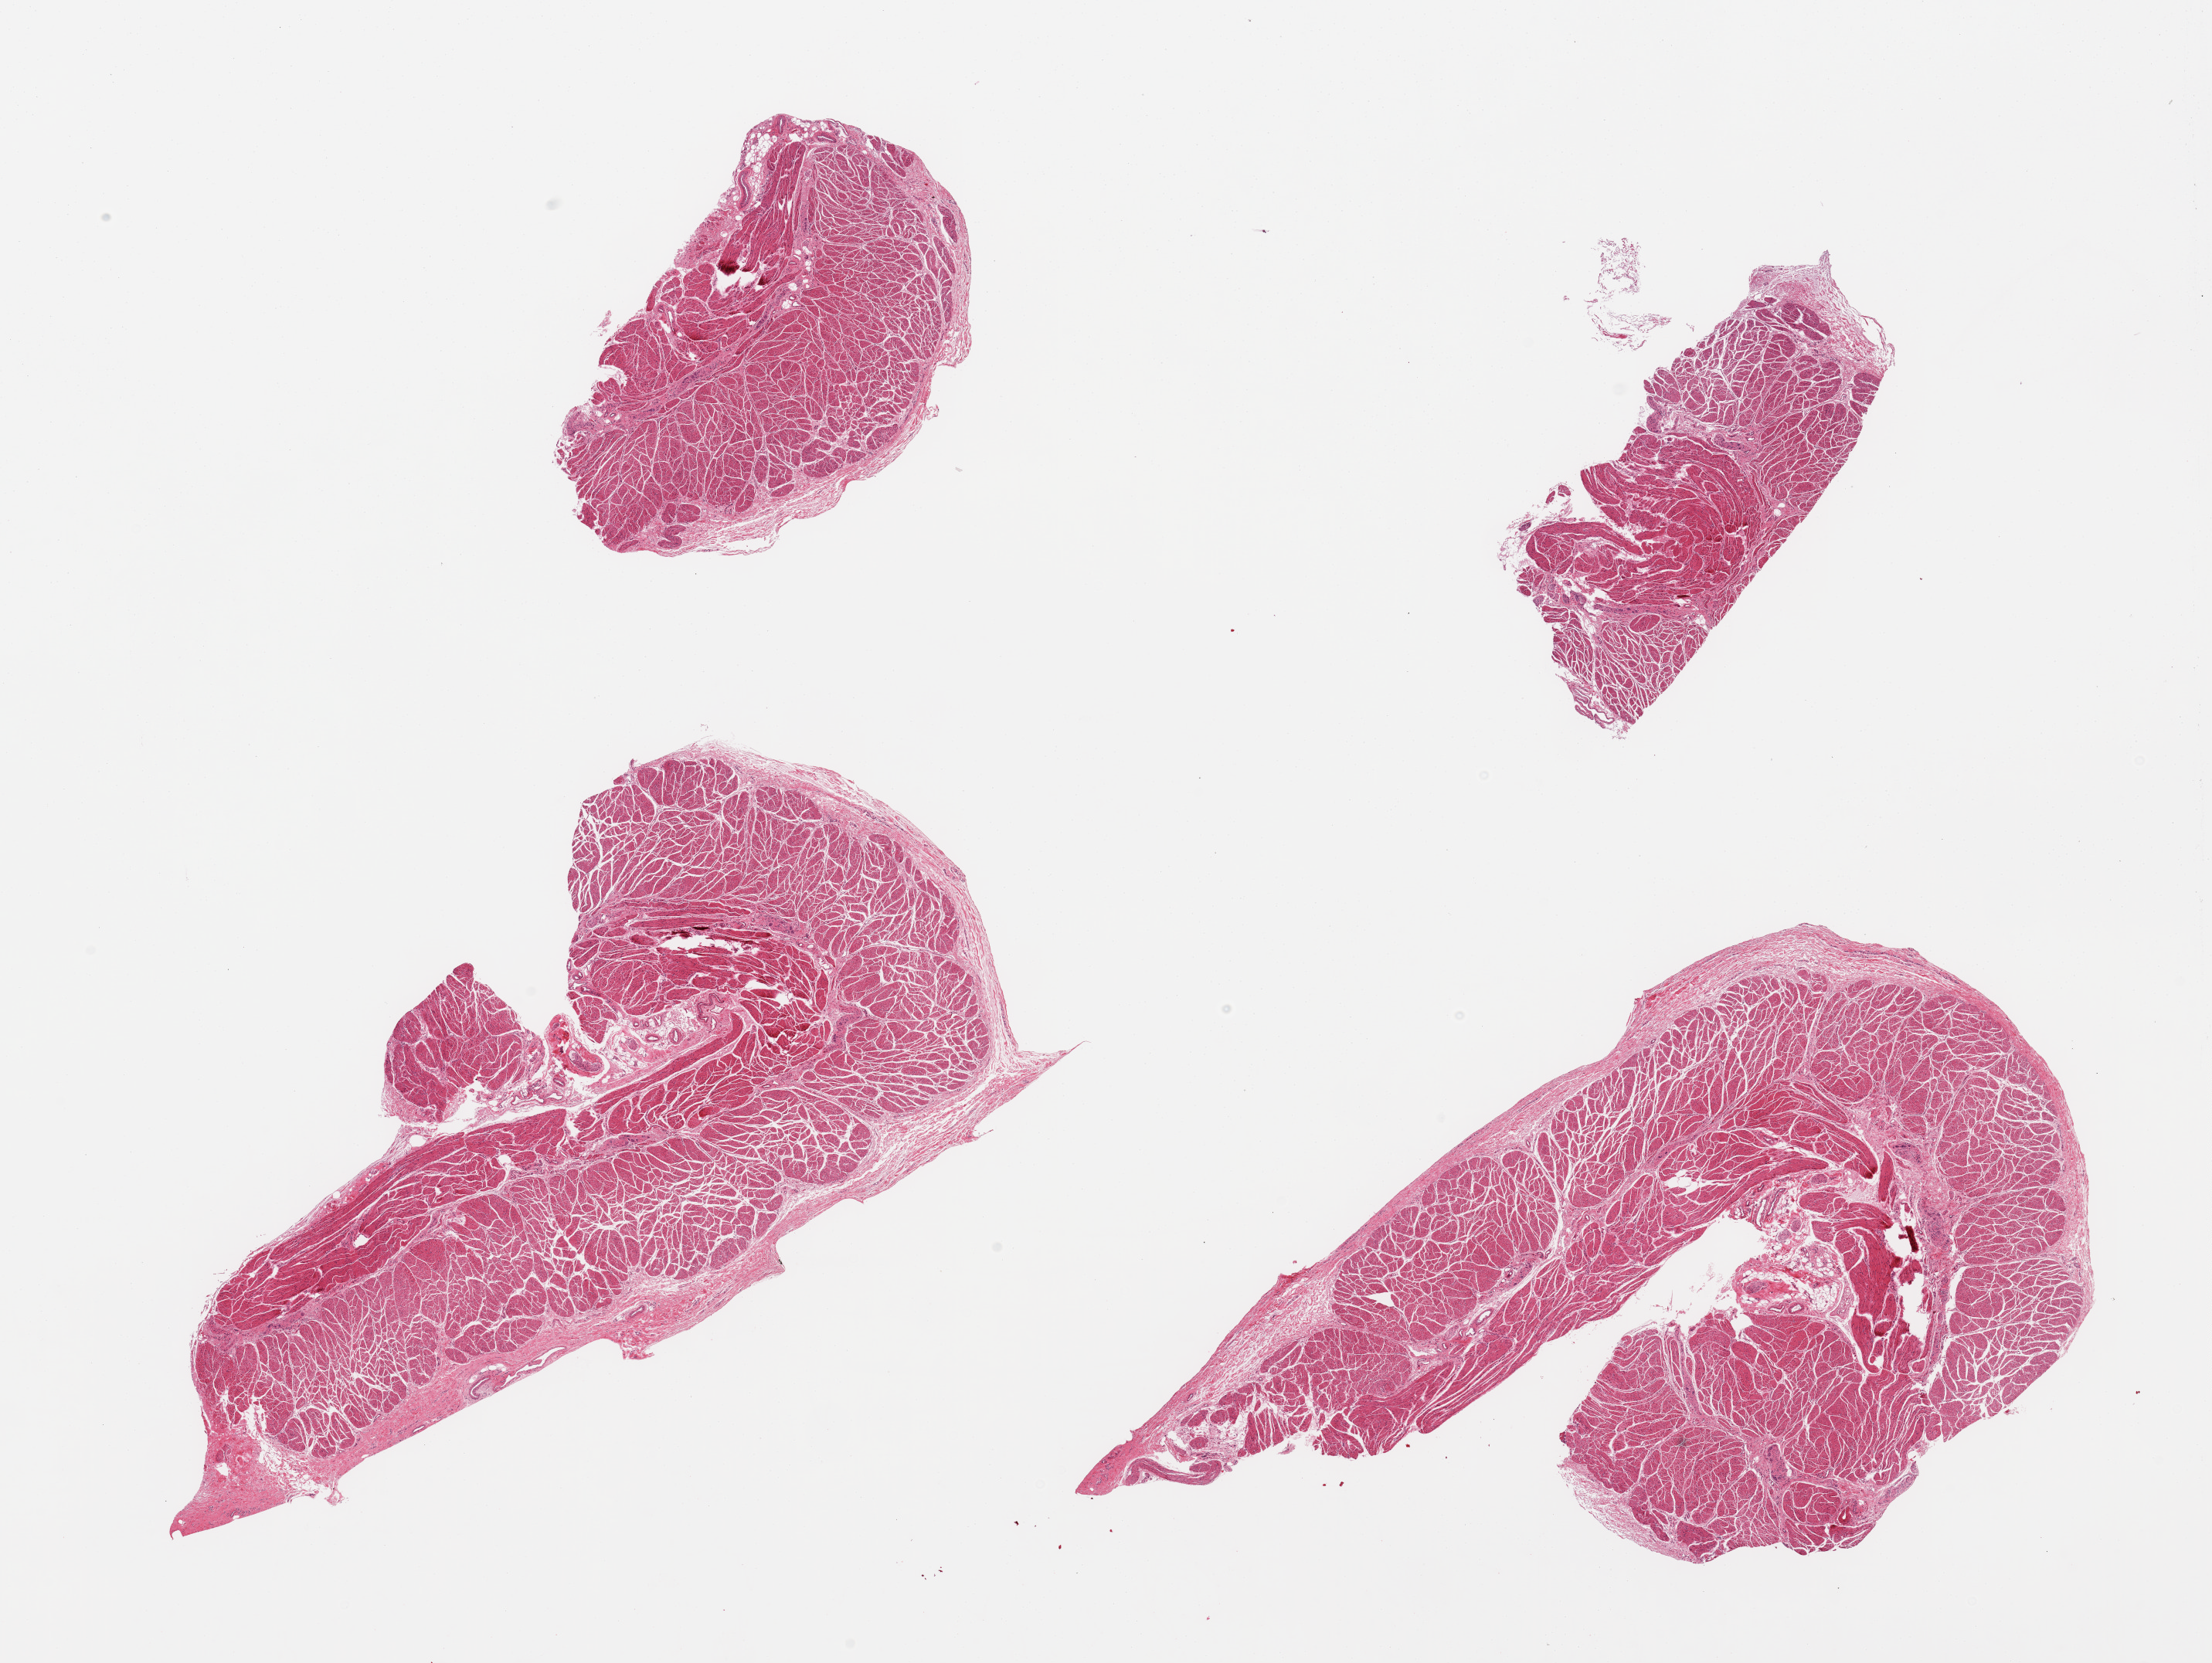
H&E whole-slide image, brightfield, a low-resolution overview of the entire scanned area, about 22.6 x 17.0 mm; PAXgene-fixed paraffin-embedded (PFPE) section; target tissue: gastroesophageal junction; donor tissue sample. Donor sex: male.
Reviewer comment on this tissue sample: 4 pieces, target muscularis.